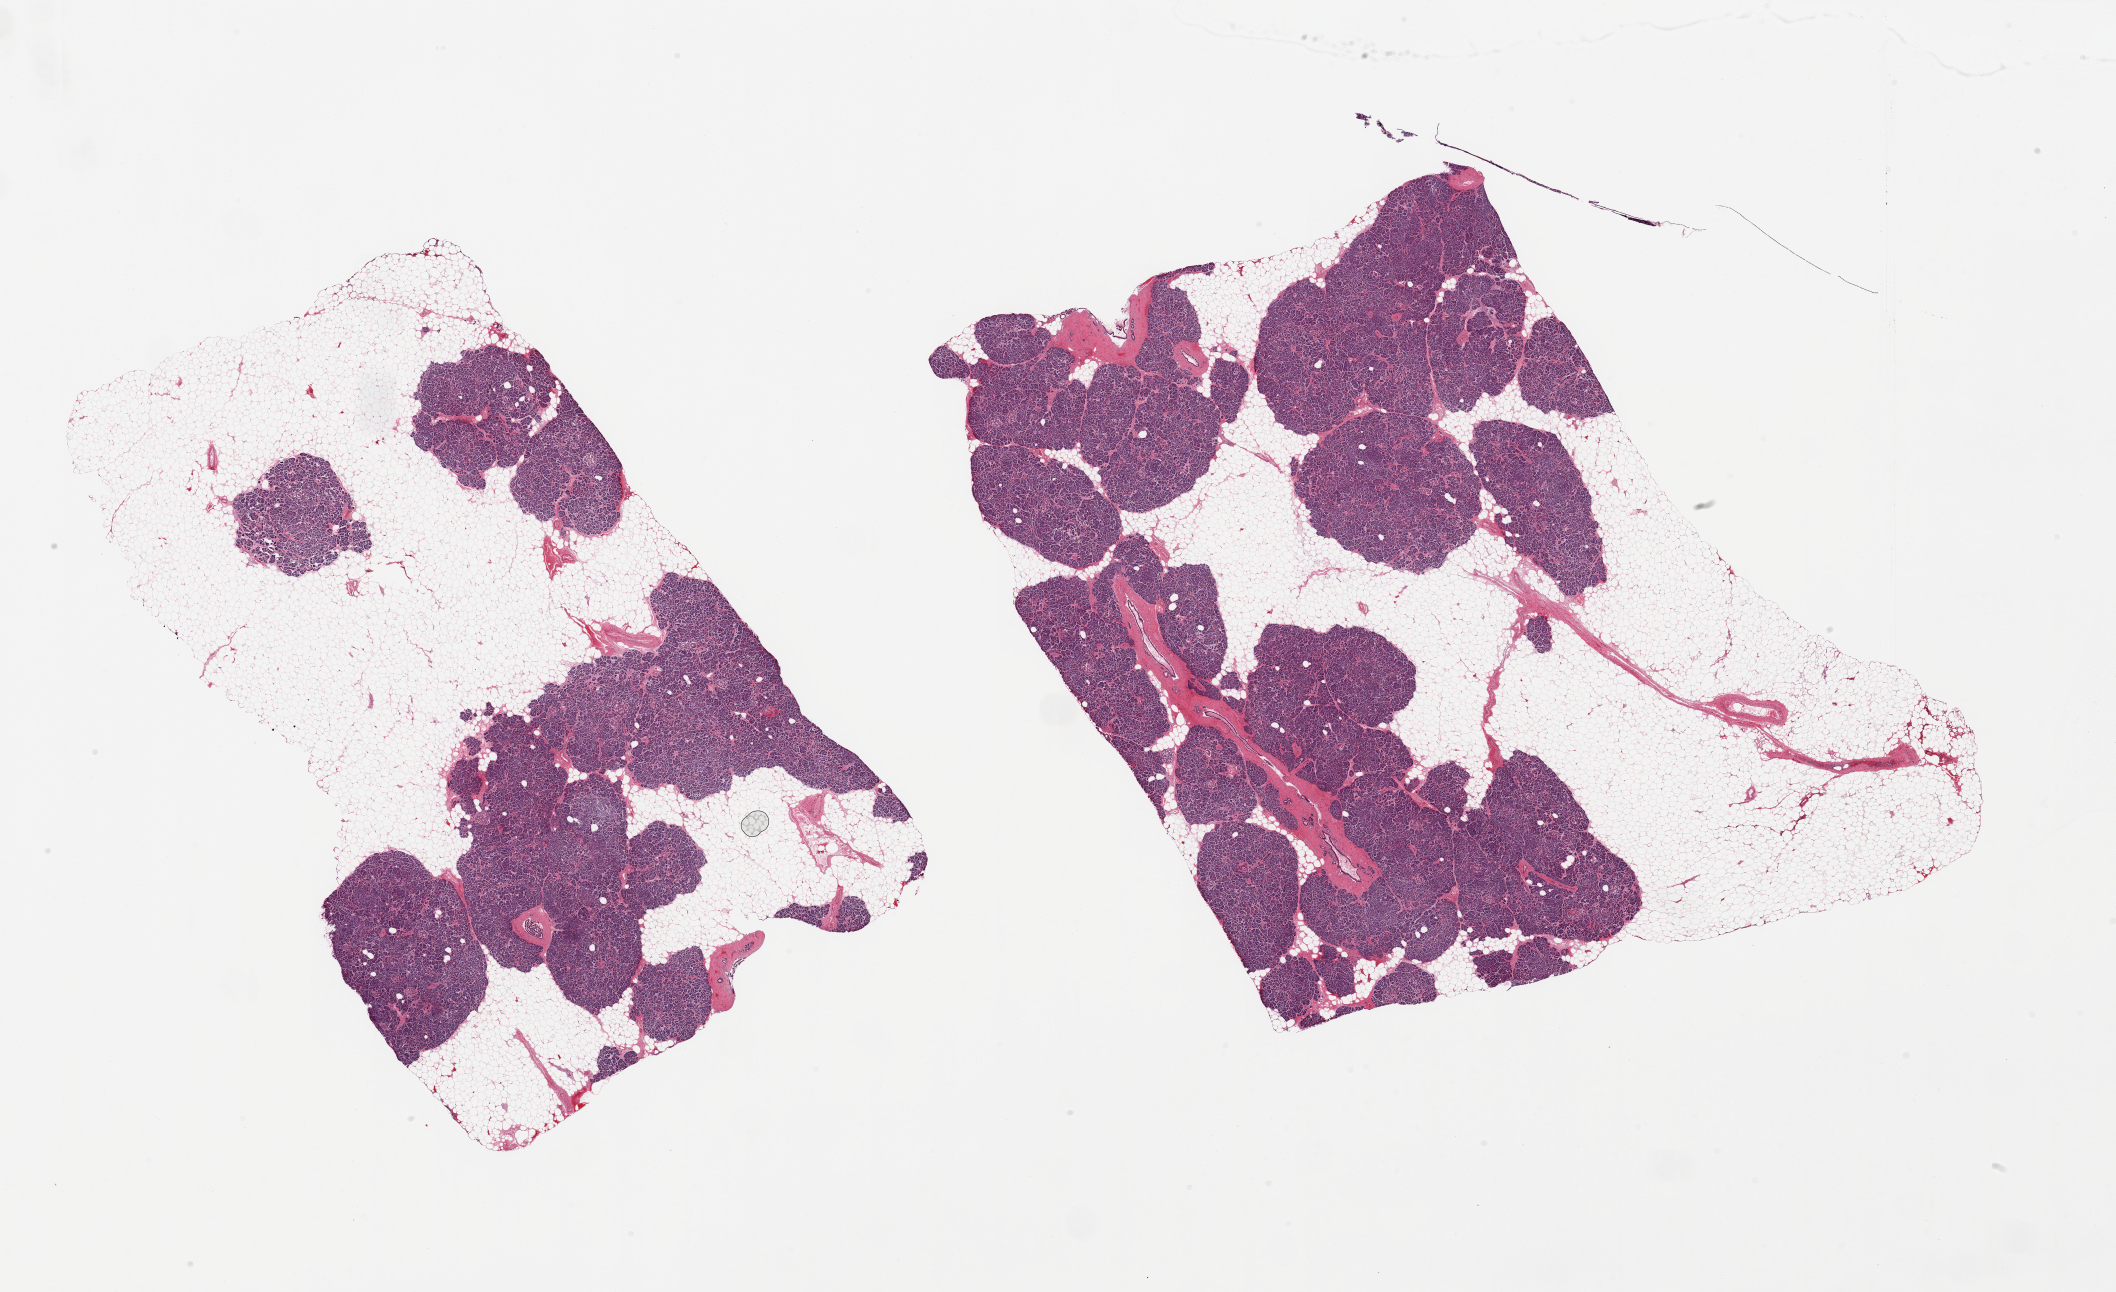
Hematoxylin and eosin (H&E) whole-slide image — whole scanned area (about 33.5 x 20.4 mm) shown as a low-resolution overview, PAXgene-fixed, paraffin-embedded tissue, target tissue: pancreas, tissue donor sample. Donor: male.
• review note (as recorded): 1 pieces; 50% internal fat